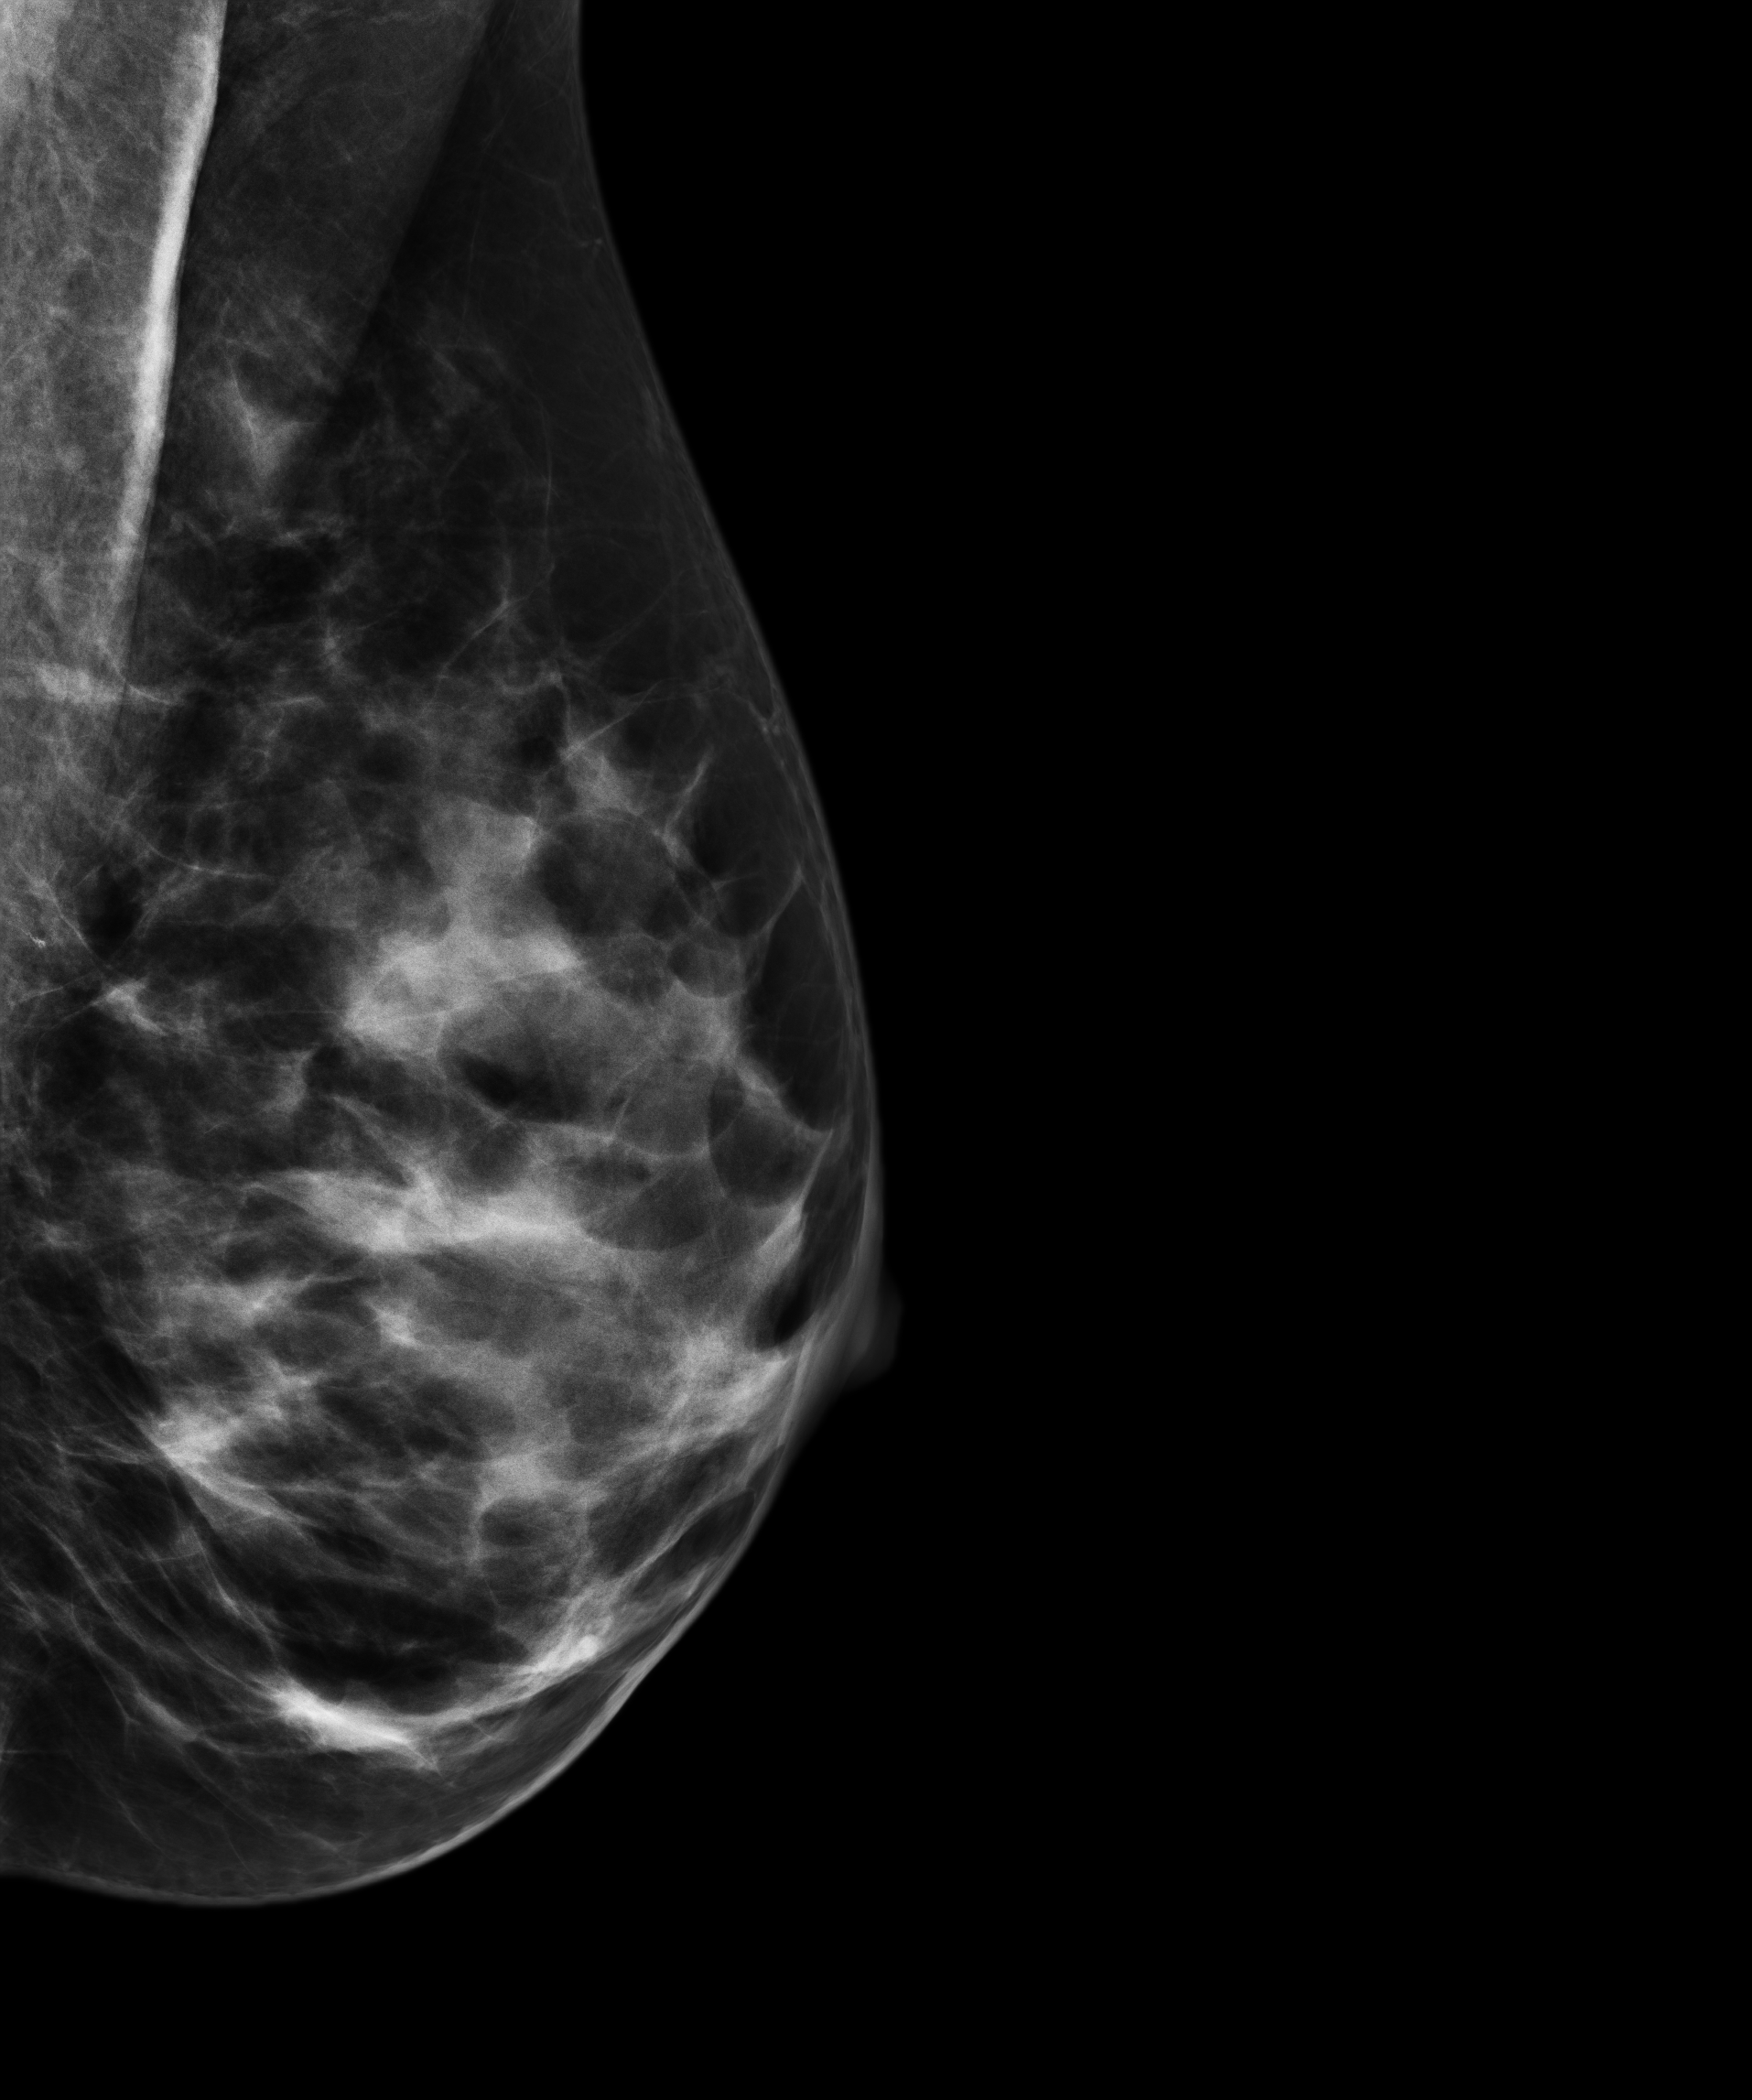
Digital mammogram (FFDM); left breast; ML view; diagnostic examination (additional views); system: Senographe Essential VERSION ADS_54.11. Female patient, age 54 years.
Breast density at the screening exam (both breasts): heterogeneously dense (BI-RADS density category c). Final BI-RADS category for the screening round (tomosynthesis exam, both breasts): category 3. Recall: recalled for additional imaging after this screen.